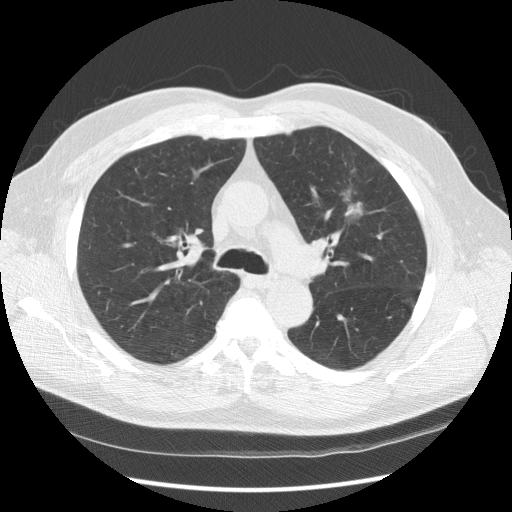
Low-dose screening chest CT, axial slice, second annual screen, lung window (W 1500 / L -600 HU). Male participant, aged 65 years at enrolment. Current smoker at enrolment.
• Expert reader's lesion annotation, bounding box (x1, y1, x2, y2) in pixels: (323, 169, 381, 235).
• The screening reader recorded 2 non-calcified nodules or masses ≥4 mm on this exam (left upper lobe, right upper lobe); which of them this box marks is not recorded.
• Official screen result: positive, other.
• Lung cancer was diagnosed 120 days after this screen: carcinoma, NOS, left upper lobe, poorly differentiated (G3), stage IIIA (AJCC 6th edition), 25 mm at pathology.